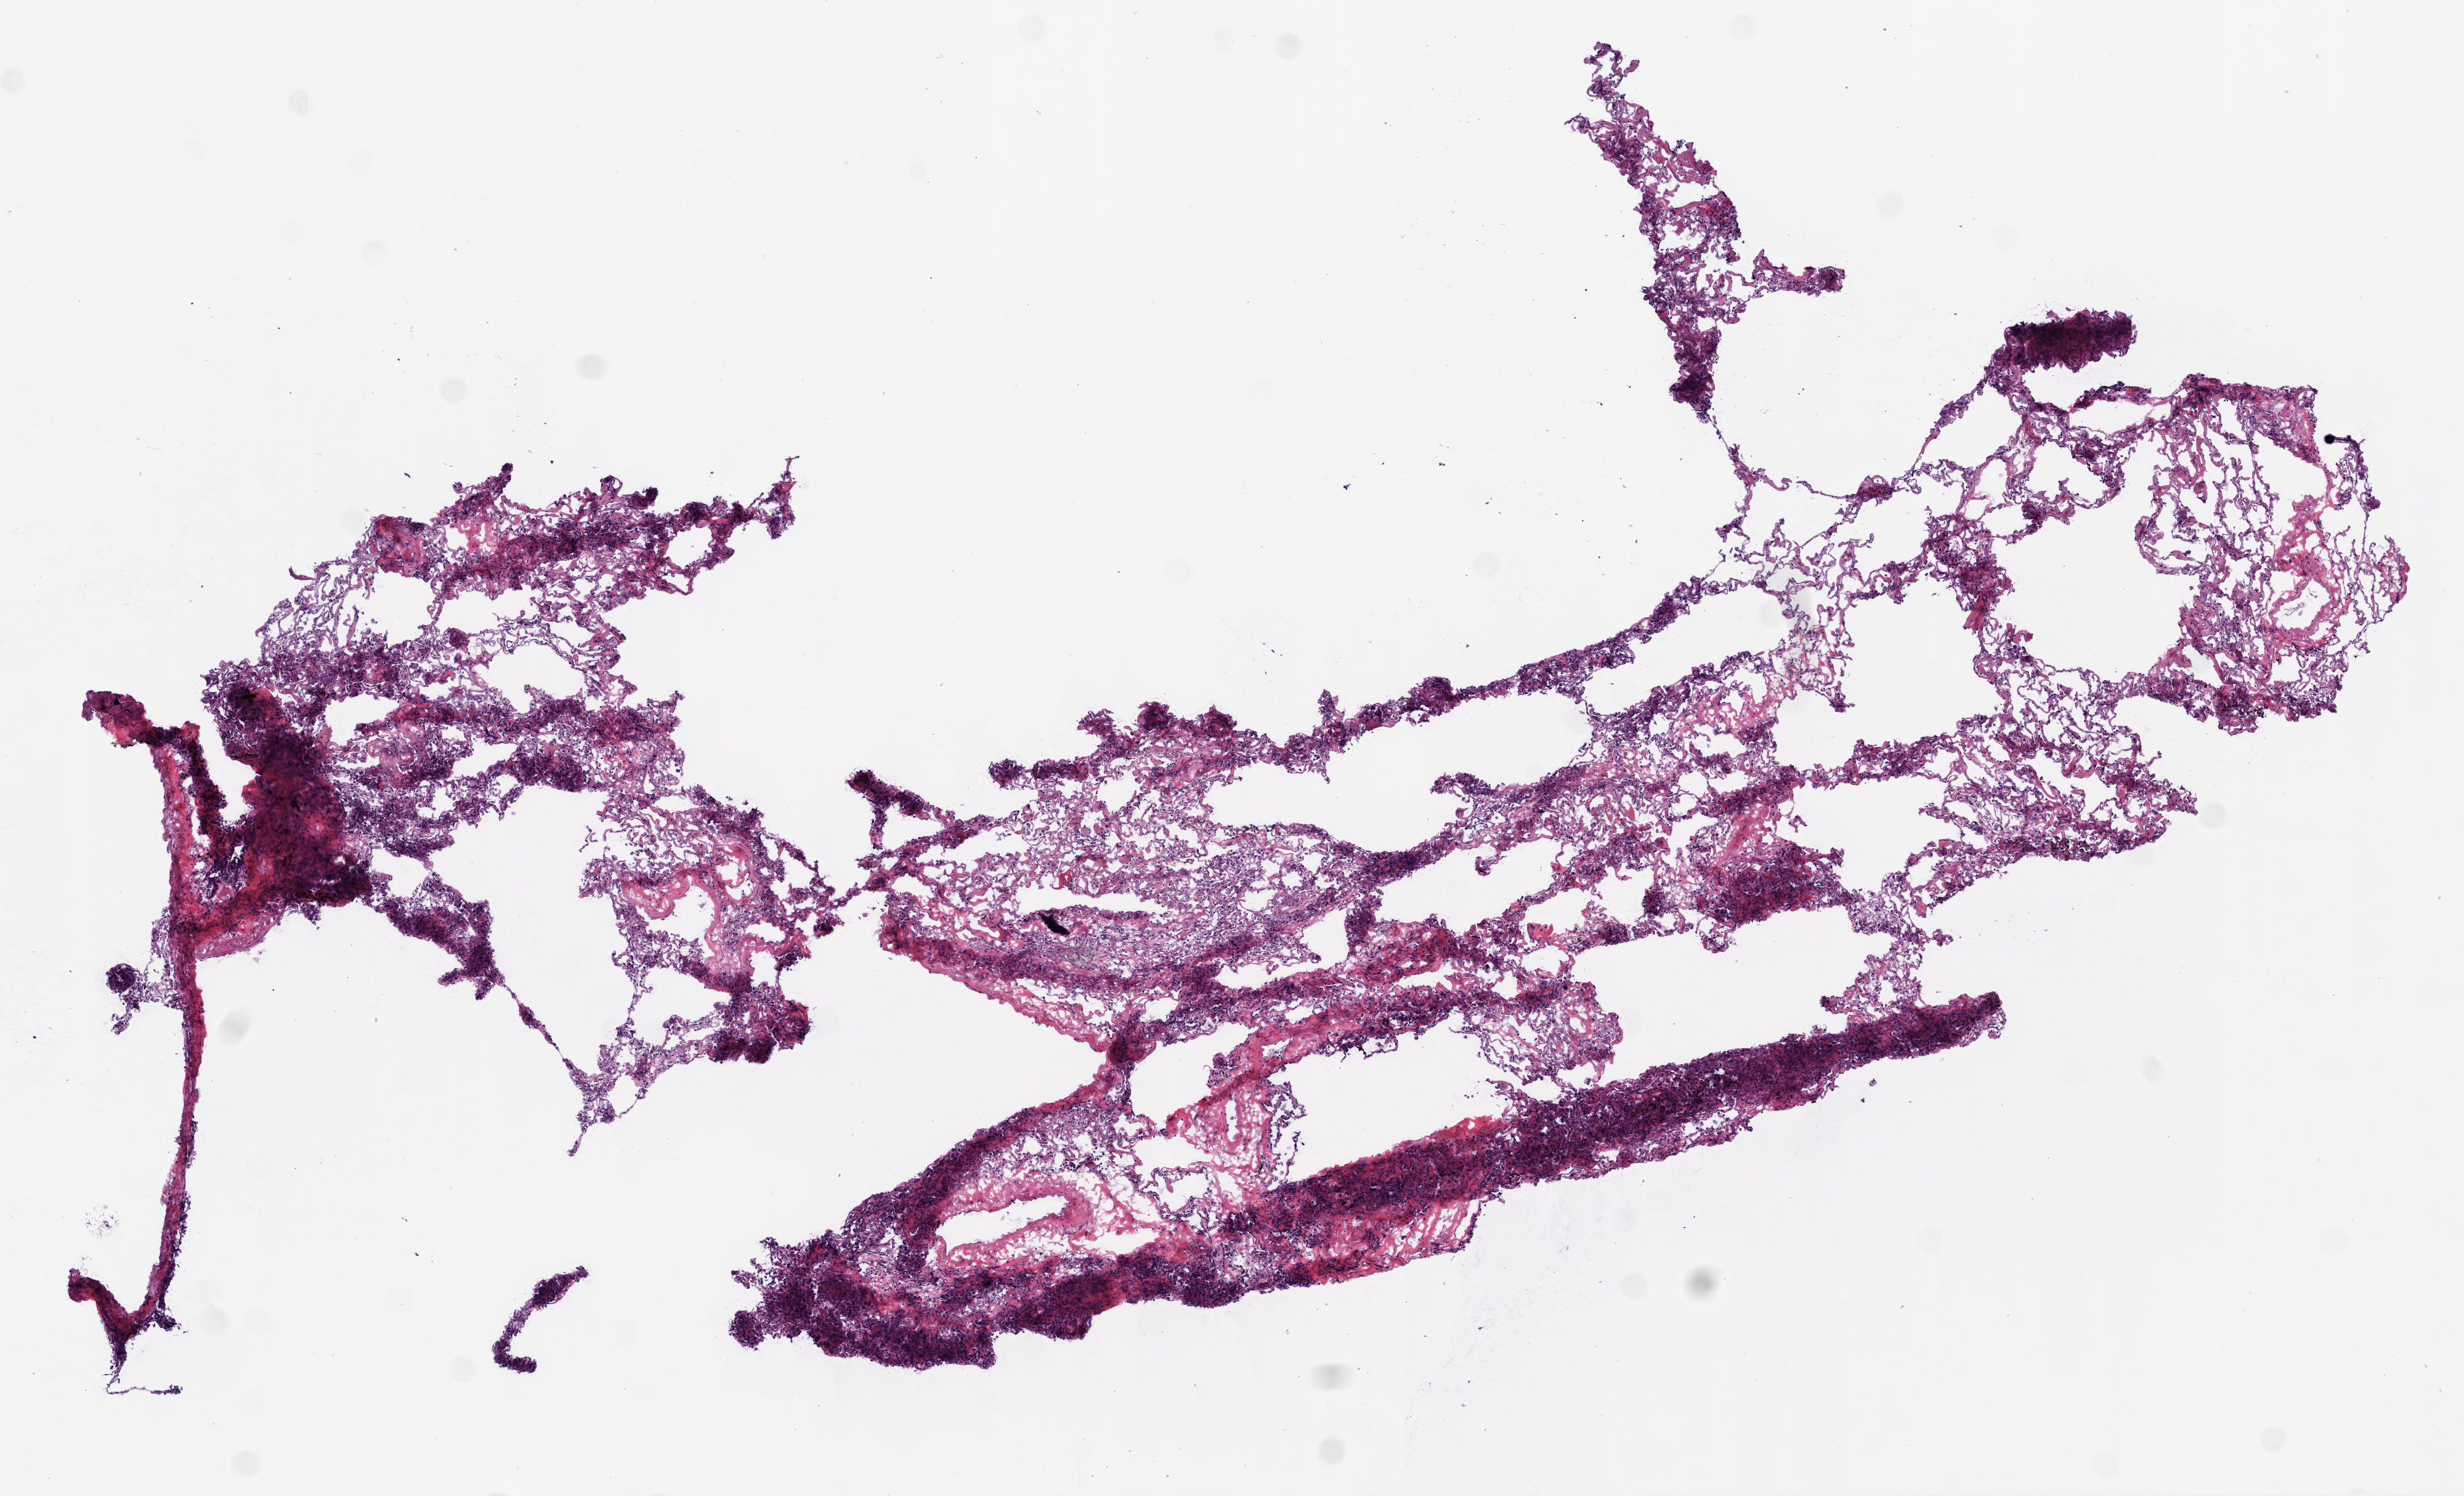
H&E whole-slide image — a low-resolution overview of the entire scanned area, about 8.0 x 4.9 mm; frozen section from the top of the tissue portion; solid tissue normal (non-tumour tissue) sample from the lung. Male patient; age at initial diagnosis 65 years.
This section: solid tissue normal sample (biorepository sample class). Patient diagnosis: Adenocarcinoma, NOS.